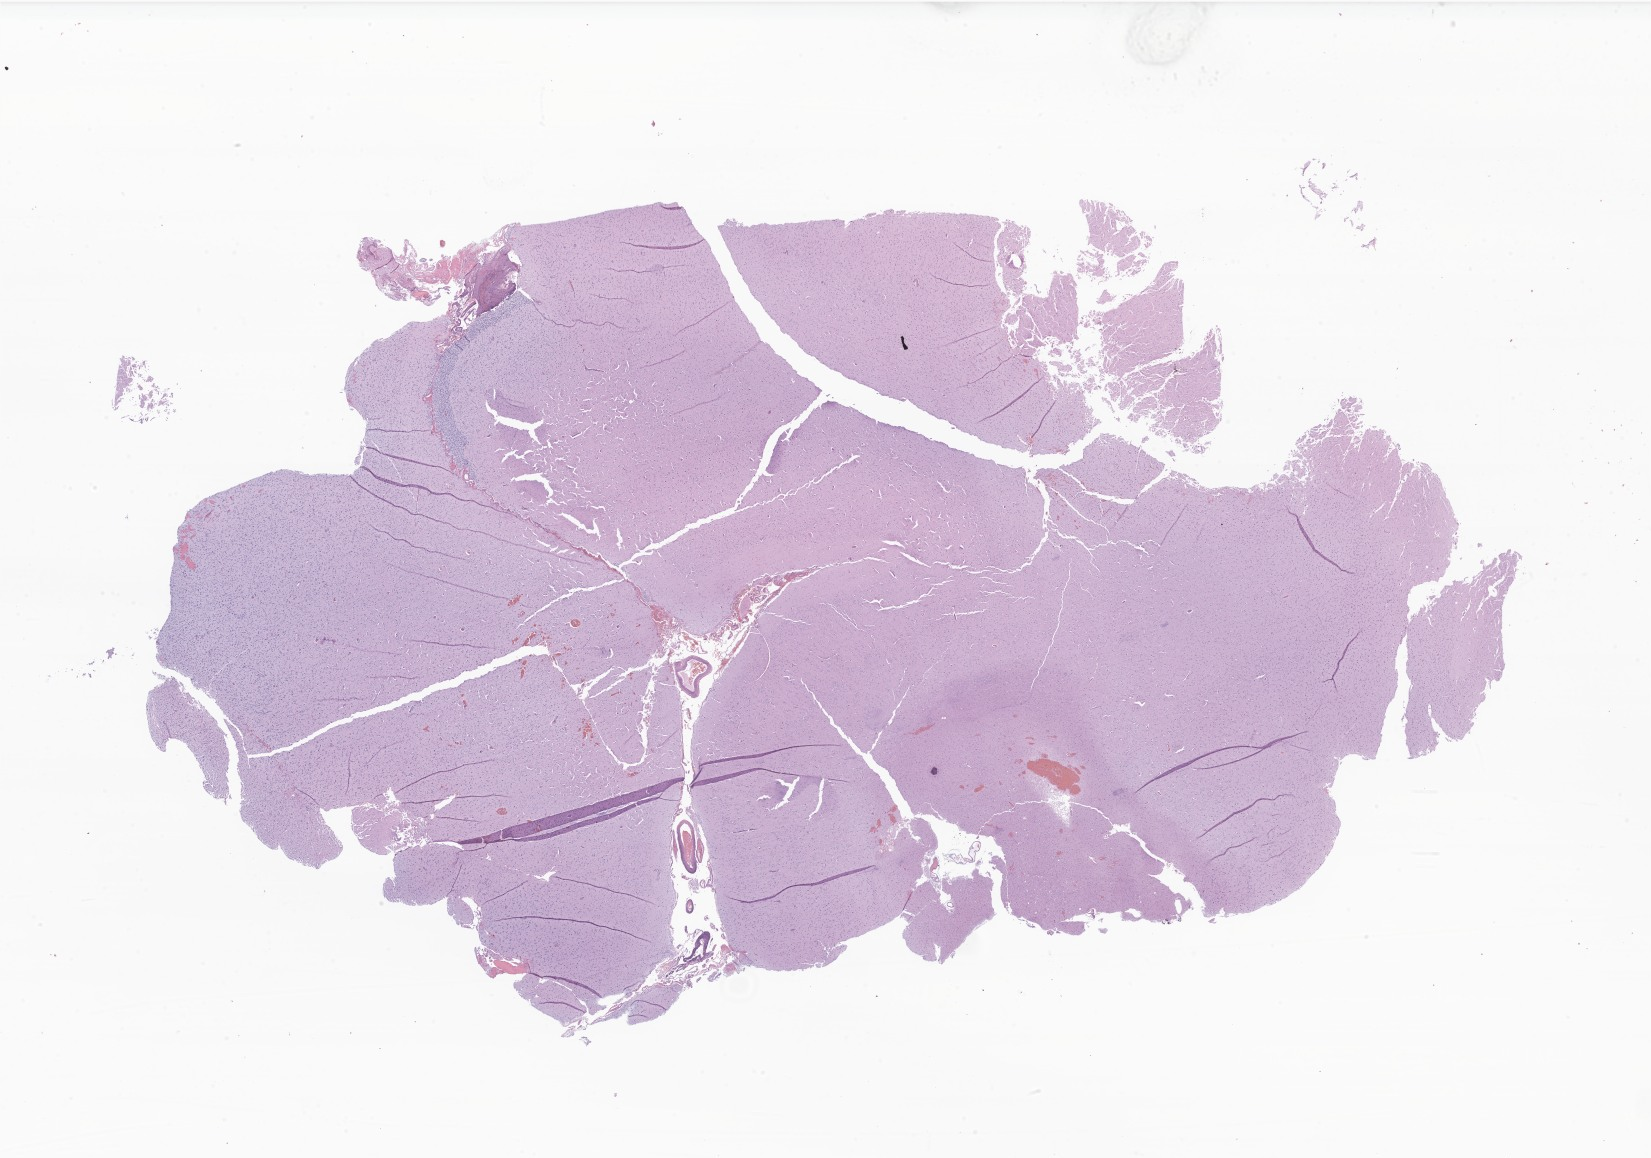
Whole-slide image, hematoxylin and eosin (H&E) stain of tumor tissue from the brain — low-resolution overview of the scanned area, about 27.8 x 19.5 mm, FFPE section. Patient male; age 229 months (19 years 1 month).
* diagnosis: Glioma, malignant